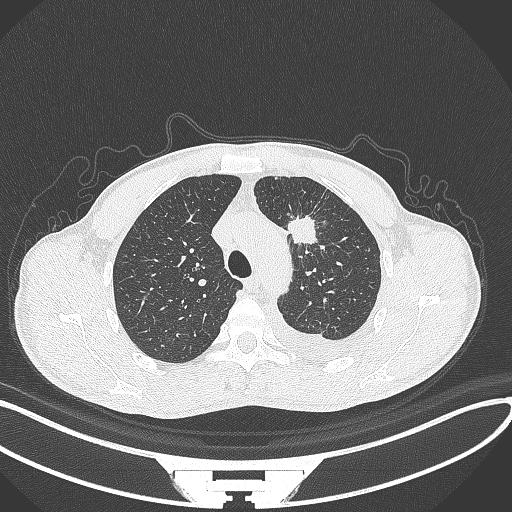
Chest CT, one axial slice; position 257 of 371 along the scan axis; reconstruction kernel B70f; 120 kVp; lung window (W 1500 / L -600 HU); 1 mm slice thickness; 512 × 512 image matrix, field of view 400 × 400 mm. Male patient, age 49 years. Case-level facts recorded for this patient, not image findings: clinical TNM (as recorded): T1c N1 M1.
Structures marked on this image (rectangle marked by the reading radiologist):
- lung tumour (recorded histology: adenocarcinoma): box from (x=290, y=212) to (x=320, y=246) px